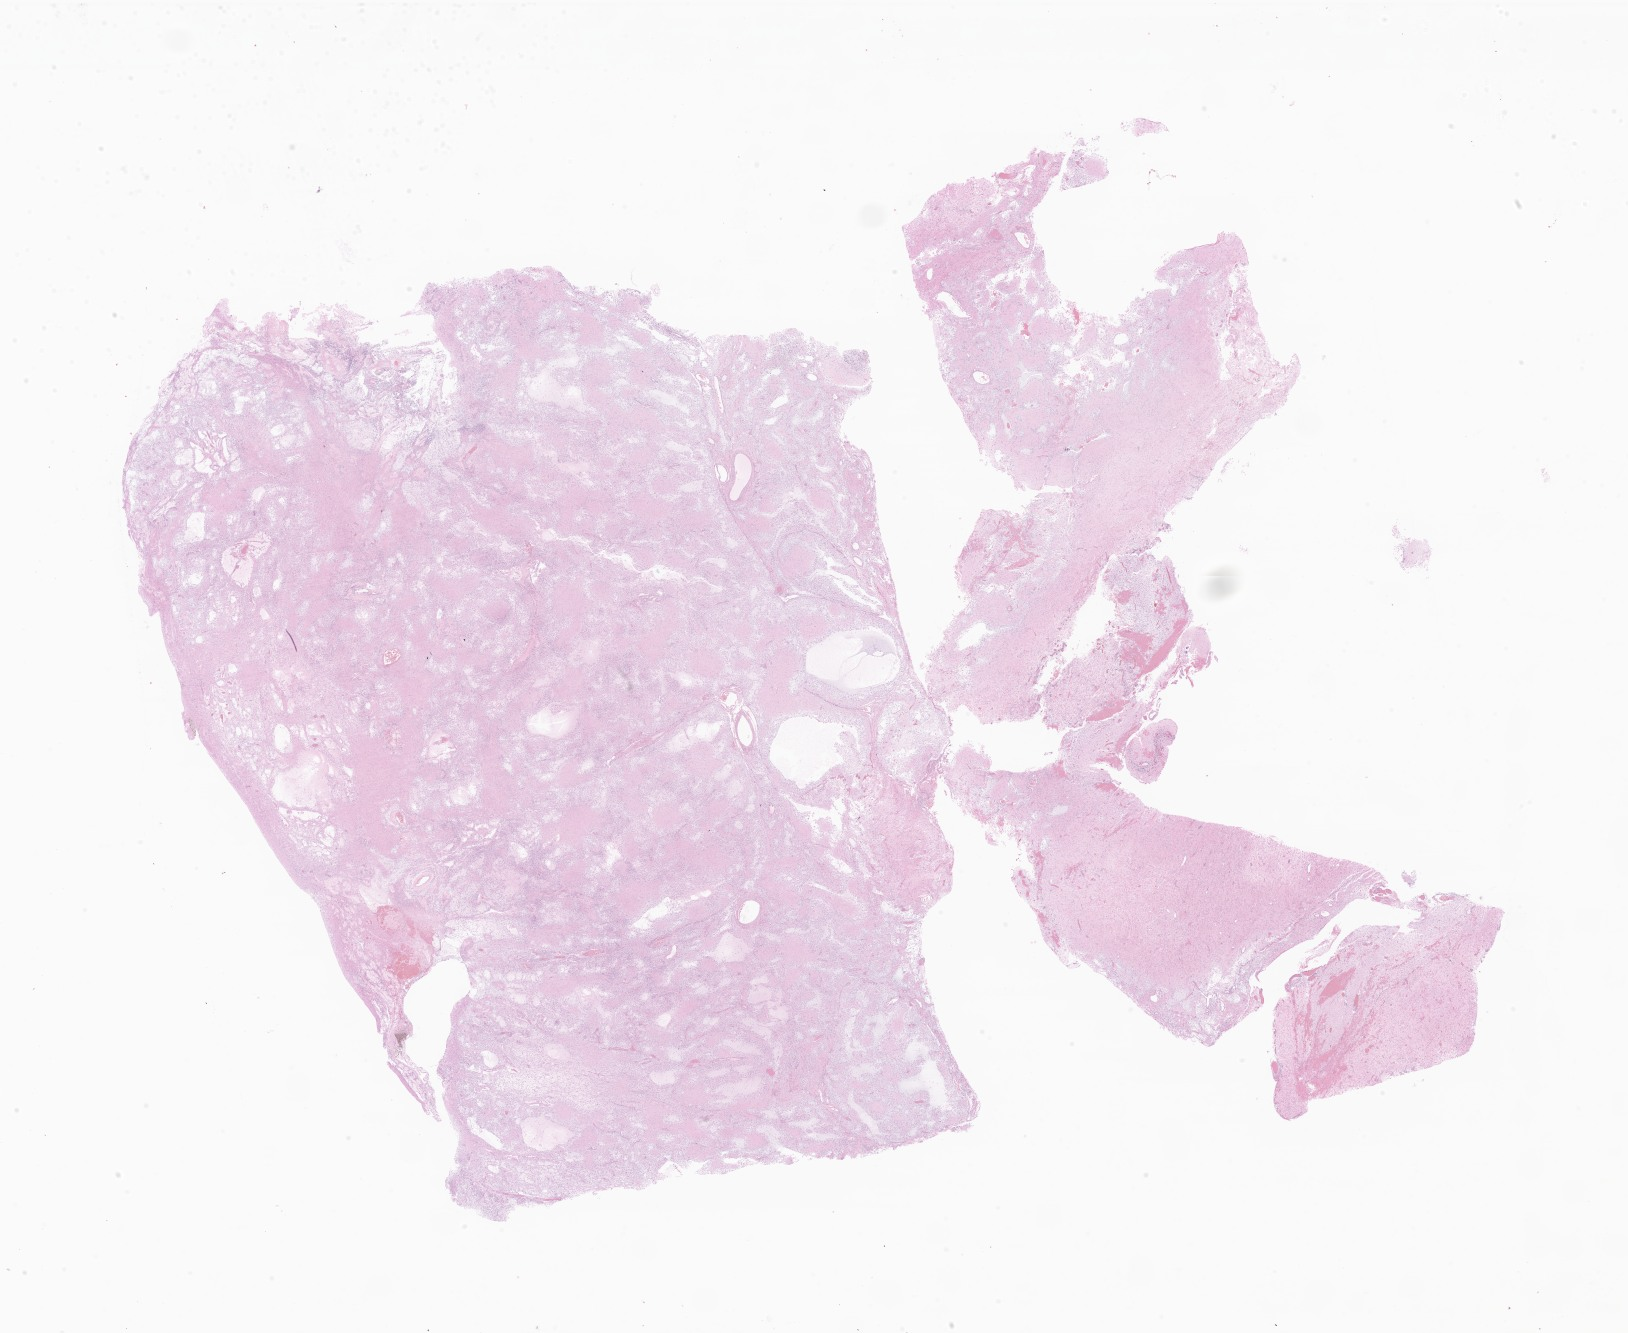
Digitized H&E-stained section of tumor tissue from the brain, shown as a low-resolution overview of the whole scanned area (about 27.5 x 22.5 mm), formalin-fixed, paraffin-embedded (FFPE) tissue. Patient male; age 66 months (5 years 6 months).
• recorded diagnosis: Glioma, malignant